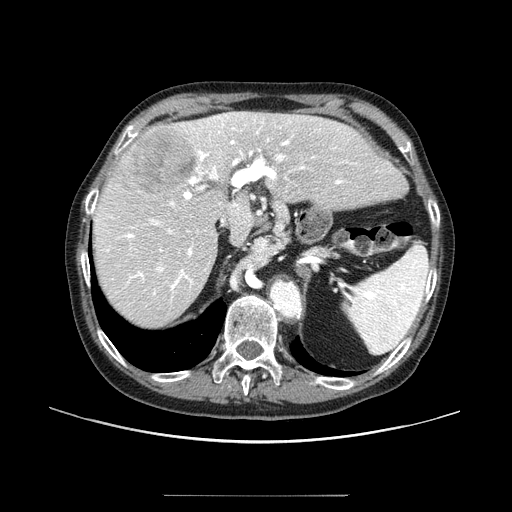
Contrast-enhanced abdominal CT (liver protocol), one axial slice; slice 63 of 91 in the series (ordered by position); 100 kVp; one of 2 acquisitions stored at this slice position; soft-tissue window (W 400 / L 40 HU); 2.5 mm slice thickness; 512 × 512 image matrix, field of view 400 × 400 mm. Case-level facts recorded for this patient, not image findings: diagnosis: hepatocellular carcinoma (patient treated with transarterial chemoembolisation; whether this scan precedes or follows treatment is not stated here); TNM stage (as recorded): Stage-I; Child-Pugh class: A; tumour differentiation: moderately differentiated; tumour nodularity: uninodular.
Outlined on this slice (semi-automatic segmentation, software-assisted and operator-edited):
- liver parenchyma outside the tumour (the mass and vessels are separate outlines, so this box may not span the whole liver): bounding box <94,111,406,326> (left, top, right, bottom; pixels)
- mass: <112,126,196,195>
- liver vessels: <96,113,356,295>